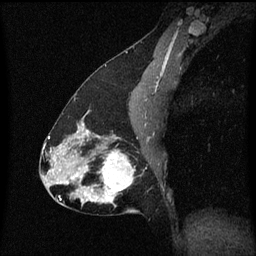
Breast MRI (dynamic contrast-enhanced), one sagittal slice. Position 31 of 60 along the scan axis. Dynamic contrast-enhanced series, image 2 of 3 at this slice position (ordered by acquisition). 1.5 T. TE 4.2 ms, TR 8.4 ms. 2 mm slice thickness. 256 × 256 image matrix, field of view 200 × 200 mm. Patient: female, 47 years.
Annotated regions visible in this slice (semi-automatic segmentation, software-assisted and operator-edited):
- analysis volume of interest (the breast-tissue region the enhancement analysis was run in; not a lesion): box from (x=81, y=138) to (x=144, y=213) px
- tumour enhancement mask (voxels above the 70 % enhancement threshold inside the analysis volume of interest): (x=81, y=138)–(x=134, y=203)